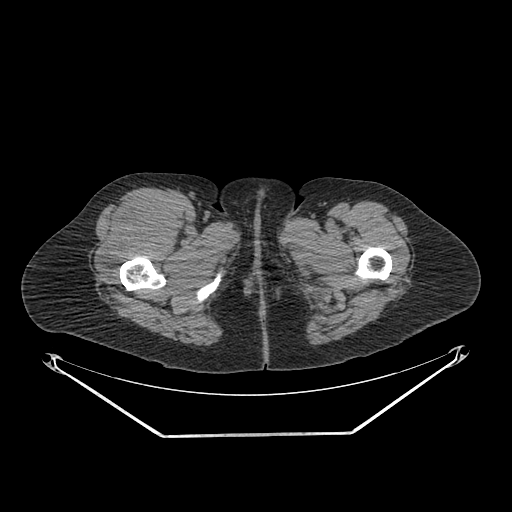
CT of an extremity soft-tissue mass (from a PET/CT study), one axial slice. Position 276 of 311 along the scan axis. Reconstruction kernel SOFT. 140 kVp. Soft-tissue window (W 400 / L 40 HU). 3.75 mm slice thickness. 512 × 512 image matrix, field of view 500 × 500 mm. Female patient. From the clinical record (not read from this slice): histological type: pleiomorphic undifferentiated sarcoma; grade: high; site of the primary tumour: right quadricep.
Annotated regions visible in this slice (expert contour drawn on MRI and transferred to this co-registered scan by the dataset authors):
- tumour plus oedema (research contour): bounding box [x1, y1, x2, y2] px = [98, 196, 174, 273]
- tumour (research contour): [98, 196, 174, 273]